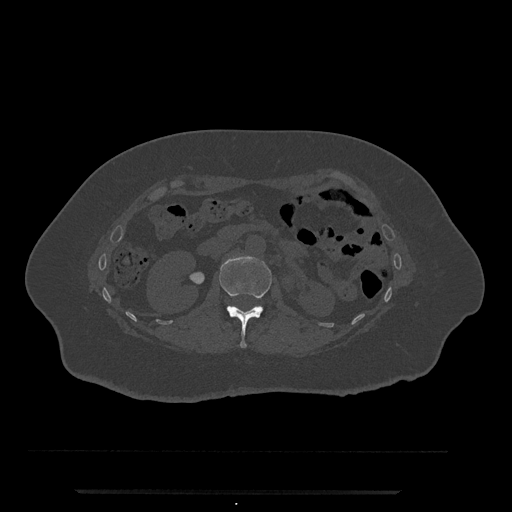
CT including the spine, one axial slice; slice 95 of 797 in the series (ordered by position); 120 kVp; bone window (W 1800 / L 400 HU); 0.5 mm slice thickness; 512 × 512 image matrix. Female patient, age 51 years. Case-level facts recorded for this patient, not image findings: primary cancer: neuro; vertebrae with lytic lesions (as recorded): T8.
Annotated regions visible in this slice (semi-automatic segmentation, software-assisted and operator-edited):
- L1 vertebra: bounding box (x1, y1, x2, y2) in pixels: (219, 255, 272, 348)